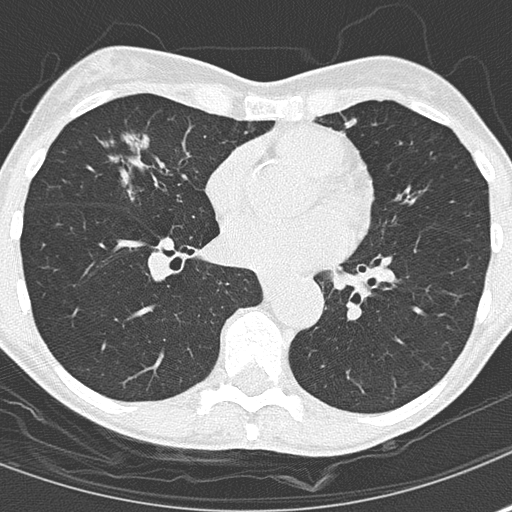
Low-dose screening chest CT, axial slice; second annual screen; lung window (W 1500 / L -600 HU); 2 mm slice thickness; lung (sharp) reconstruction kernel (B50f). Female participant, aged 67 years at enrolment. Current smoker at enrolment.
Lesion marked by an expert reader, box from (x=83, y=119) to (x=183, y=209) px. The screening reader recorded 2 non-calcified nodules or masses ≥4 mm on this exam (right middle lobe, right middle lobe); which of them this box marks is not recorded. Official screen result: positive, other. Participant outcome: lung cancer diagnosed 475 days after this screen — bronchiolo-alveolar adenocarcinoma, NOS, right middle lobe, well differentiated (G1), stage IA (AJCC 6th edition), 25 mm at pathology.